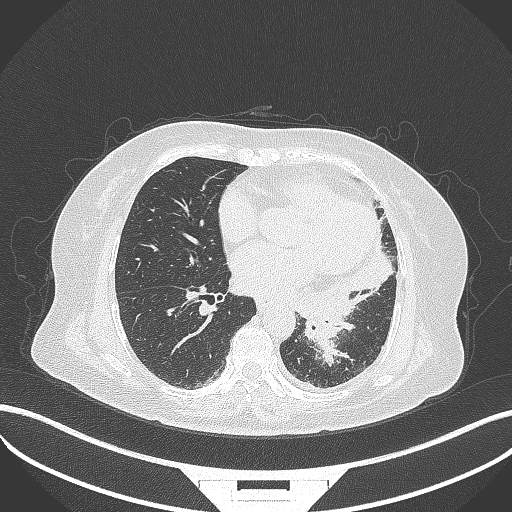
Chest CT, one axial slice; slice 153 of 322 in the series (ordered by position); reconstruction kernel B70f; lung window (W 1500 / L -600 HU); 1 mm slice thickness; 512 × 512 image matrix. Female patient, age 69 years. From the clinical record (not read from this slice): clinical TNM (as recorded): T2b N3 M1.
Annotated regions visible in this slice (bounding box drawn by a radiologist):
- lung tumour (recorded histology: adenocarcinoma): bounding box <304,307,345,342> (left, top, right, bottom; pixels)